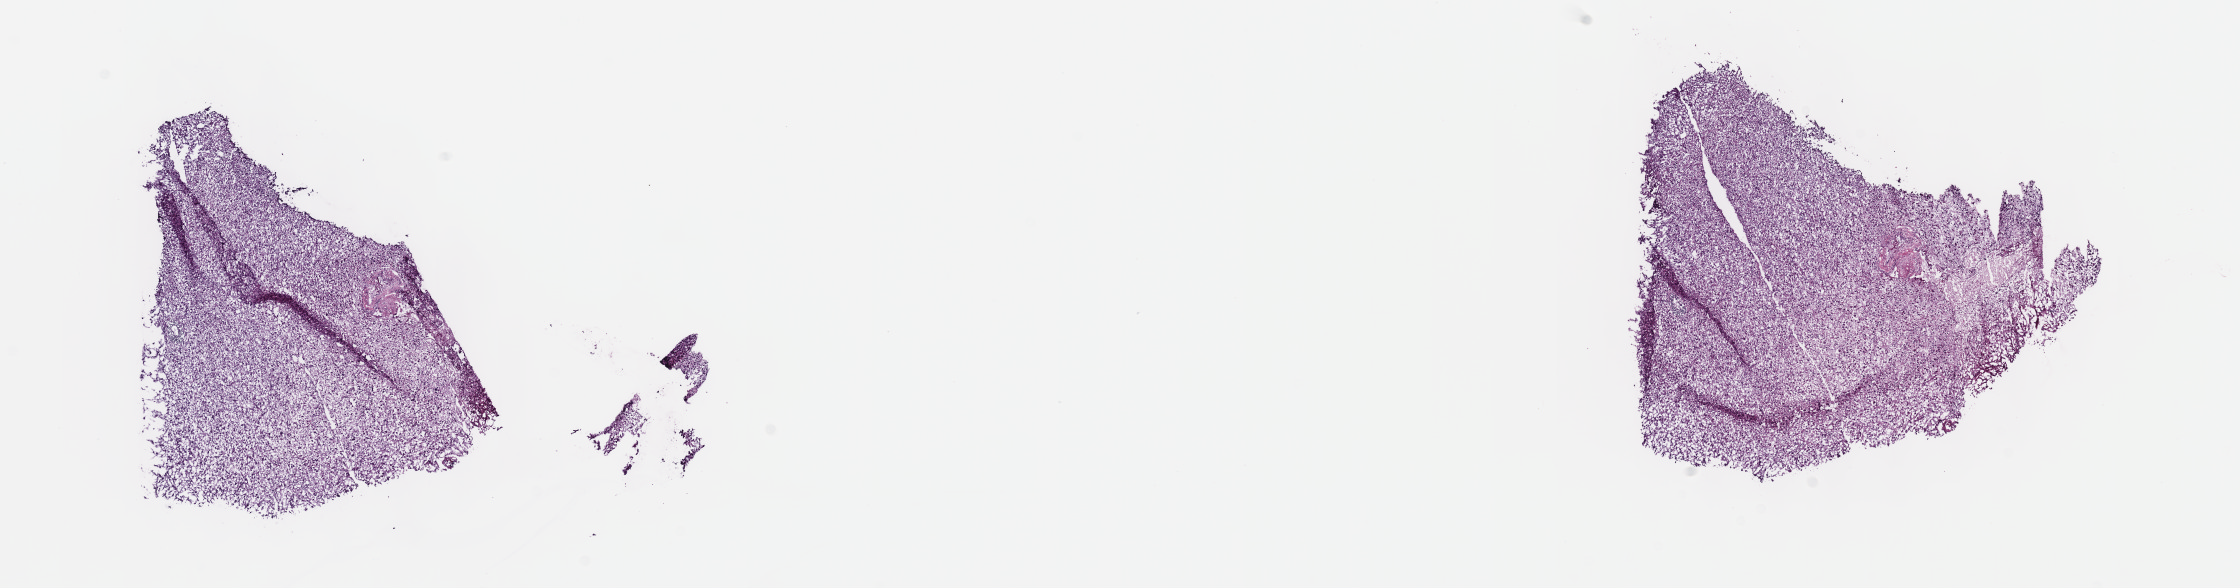
Digitized Hematoxylin and eosin (H&E) stained tissue section (whole slide) — whole scanned area (about 18.1 x 4.8 mm, from a 40x scan) shown as a low-resolution overview. Frozen section. Sample: primary tumour, brain. Female, age 58 years at initial diagnosis.
Pathologic diagnosis: Oligodendroglioma, anaplastic (cerebrum).